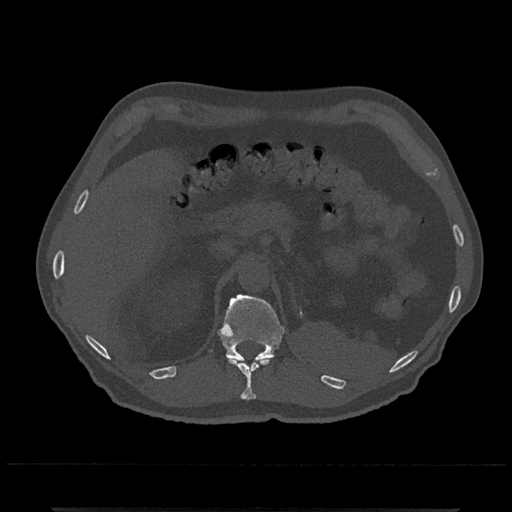
CT including the spine, one axial slice; position 453 of 797 along the scan axis; 120 kVp; bone window (W 1800 / L 400 HU); 0.5 mm slice thickness; 512 × 512 image matrix. Patient: male, 67 years. From the clinical record (not read from this slice): primary cancer: prostate.
Outlined on this slice (semi-automatically segmented with operator editing):
- T11 vertebra: bounding box <228,356,274,400> (left, top, right, bottom; pixels)
- T12 vertebra: <217,294,285,363>